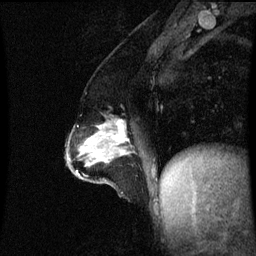
Breast MRI (dynamic contrast-enhanced), one sagittal slice; position 28 of 60 along the scan axis; dynamic contrast-enhanced series, image 2 of 3 at this slice position (ordered by acquisition); 1.5 T; TE 4.2 ms, TR 8.9 ms; 256 × 256 image matrix, field of view 200 × 200 mm. Patient: female, 47 years. Case-level facts recorded for this patient, not image findings: setting: breast cancer imaged before/during neoadjuvant chemotherapy; receptor status: HR-positive, HER2-negative.
Structures marked on this image (semi-automatically segmented with operator editing):
- analysis volume of interest (the breast-tissue region the enhancement analysis was run in; not a lesion): box from (x=71, y=120) to (x=131, y=163) px
- tumour enhancement mask (voxels above the 70 % enhancement threshold inside the analysis volume of interest): (x=116, y=124)–(x=126, y=143)